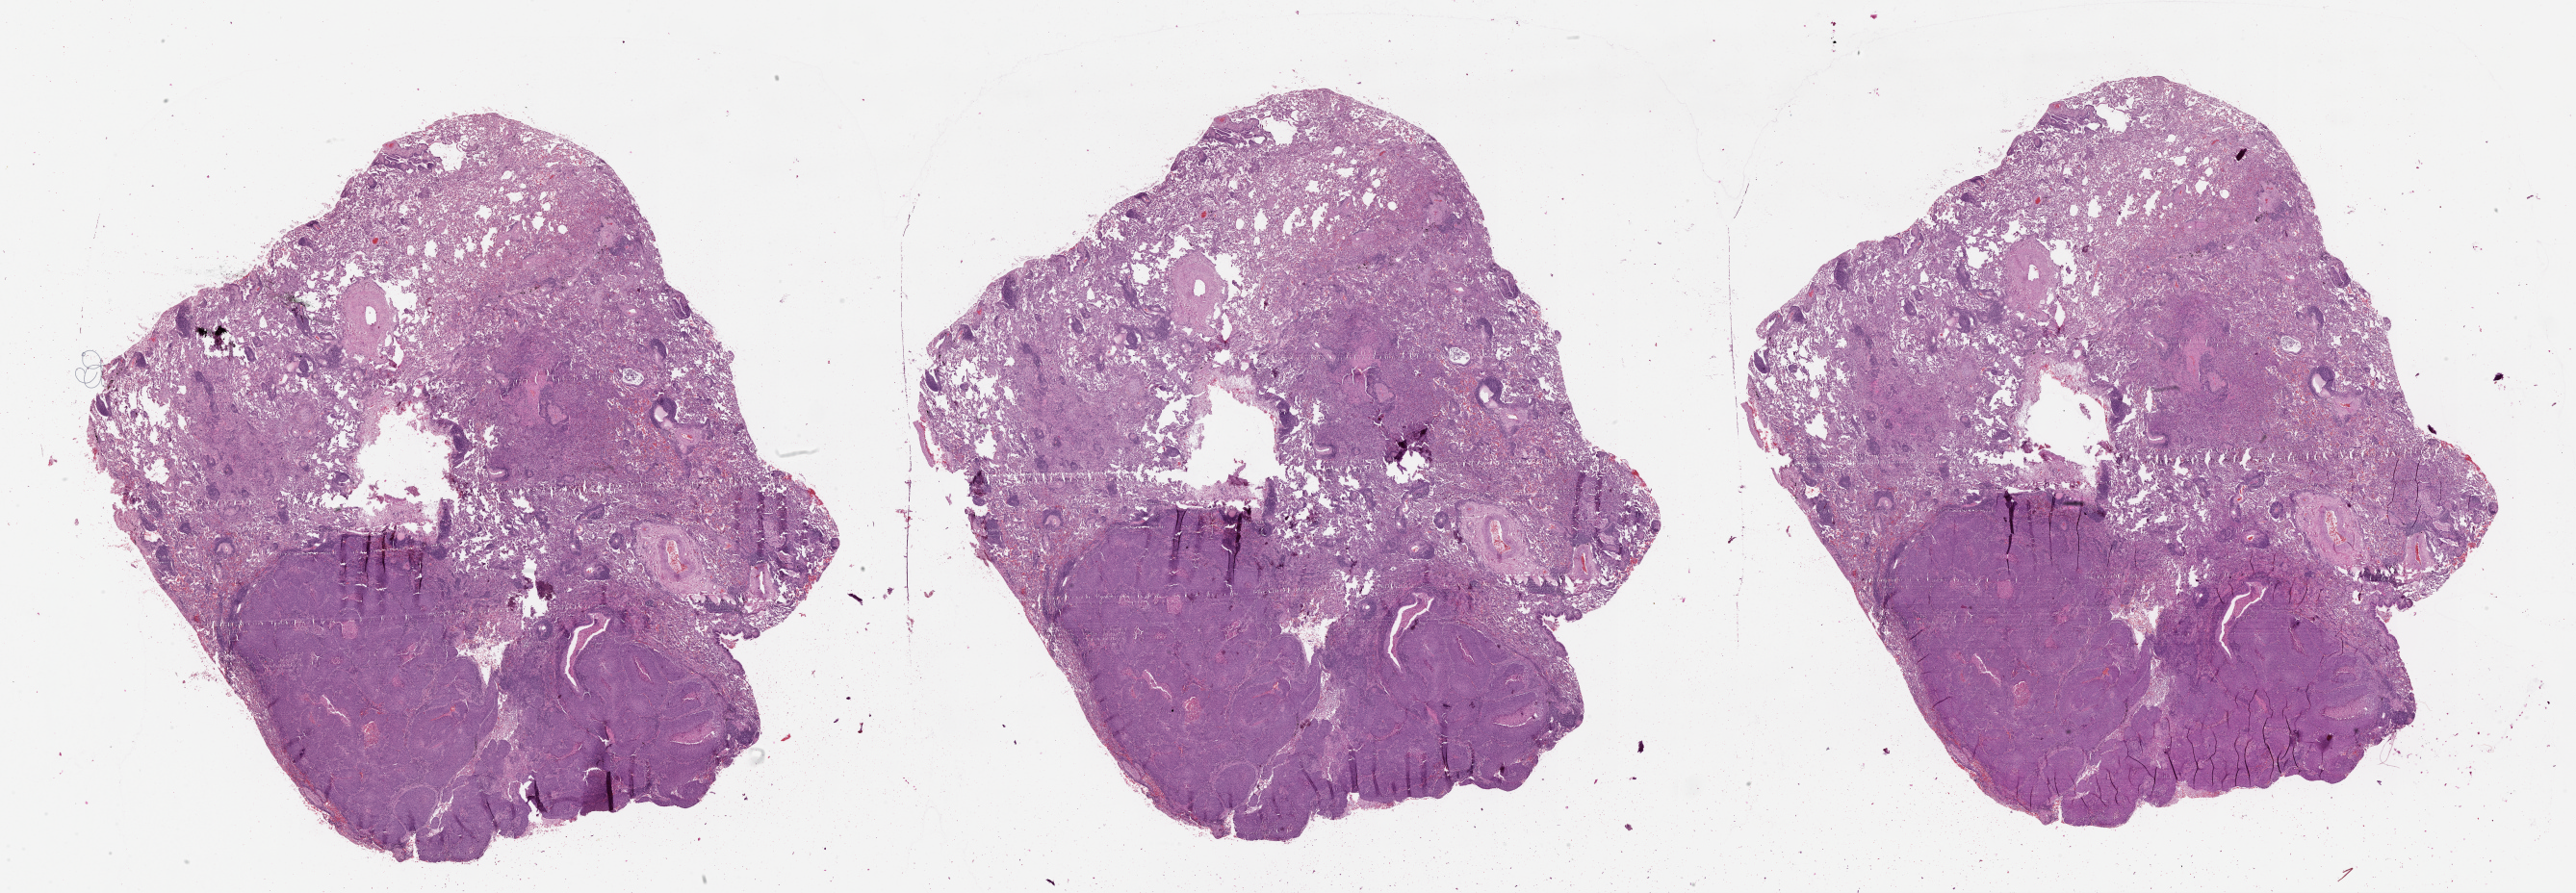
Digitized Hematoxylin and eosin (H&E) stained tissue section (whole slide), shown as a low-resolution overview of the whole scanned area (about 43.1 x 14.9 mm, acquisition: 20x scan). Tumour tissue sample, lung. 71-year-old male patient.
Patient diagnosis (cohort enrolment): squamous cell carcinoma (lung).